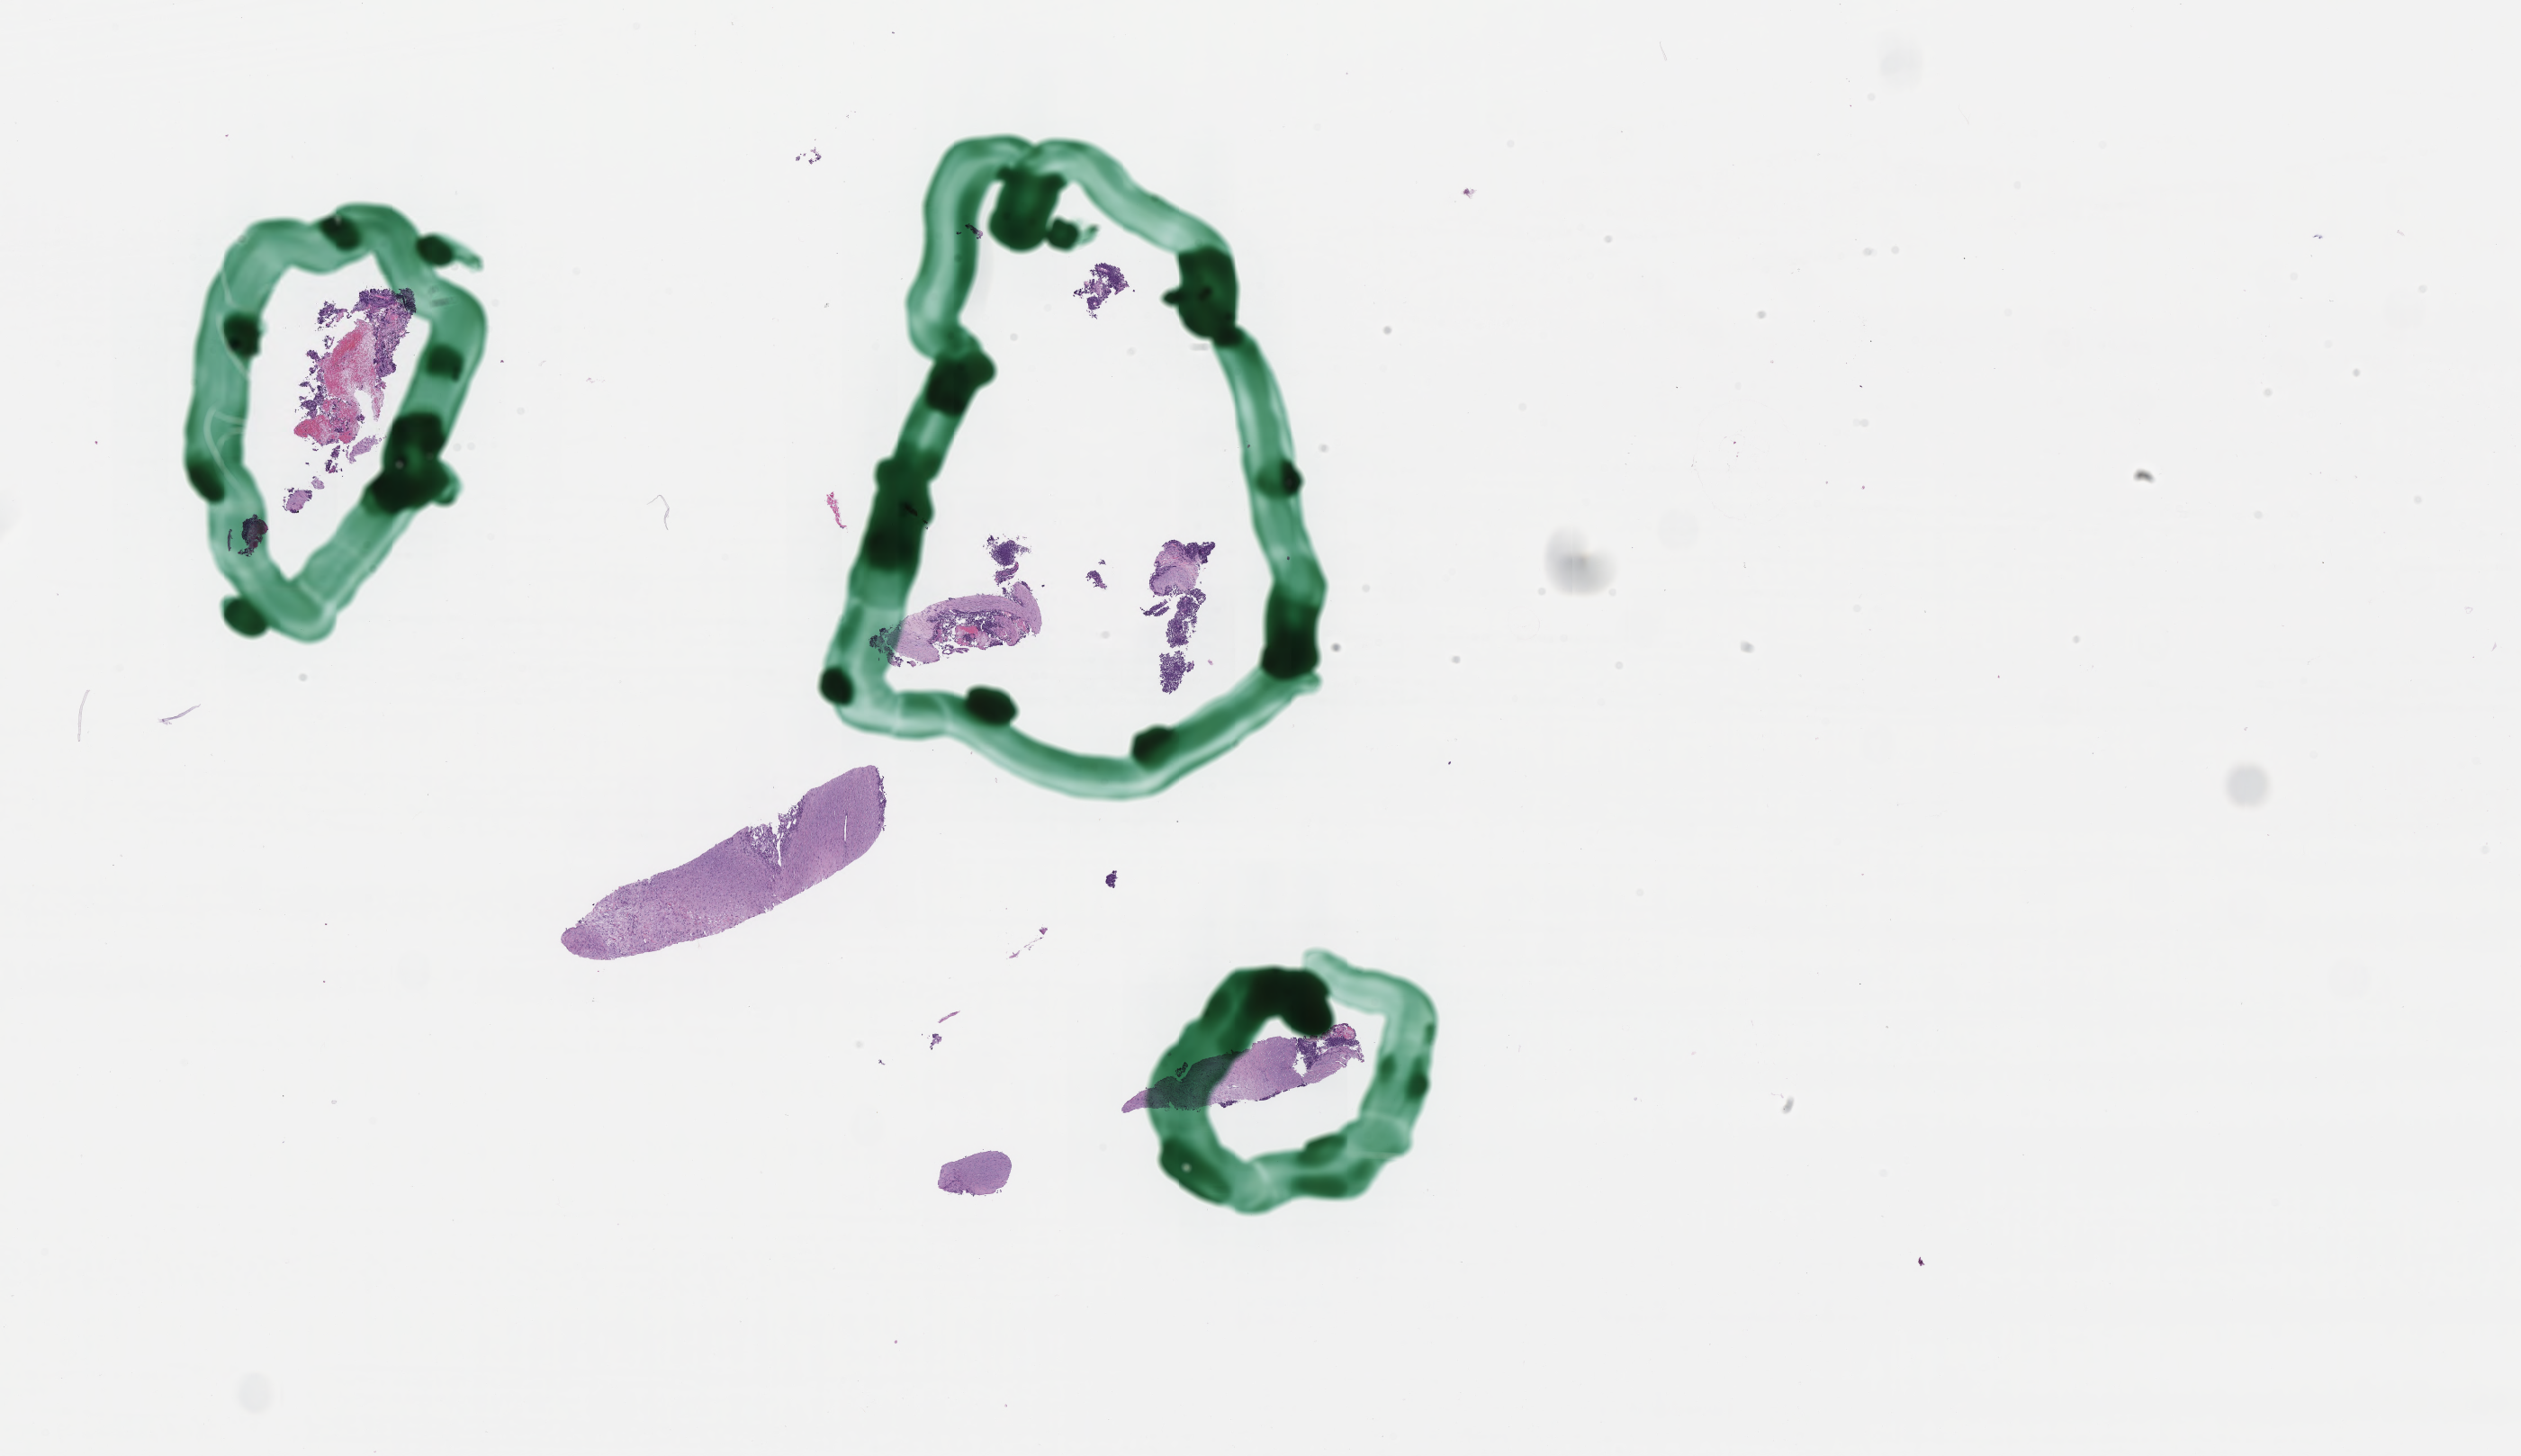
Digitized haematoxylin and eosin-stained section of tumor tissue from the abdomen, low-resolution overview of the scanned area, about 22.6 x 13.1 mm. Formalin-fixed paraffin-embedded section. Female patient, age 54 months (4 years 6 months).
Diagnosis: Neuroblastoma, NOS.